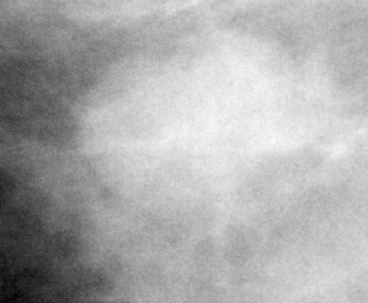
Cropped region of a digitized screen-film mammogram centred on a radiologist-marked abnormality; right breast; MLO view; BI-RADS breast density category 3 (scale 1–4).
Mass, shape oval, margins circumscribed; BI-RADS assessment category 4; pathology (as recorded): benign.